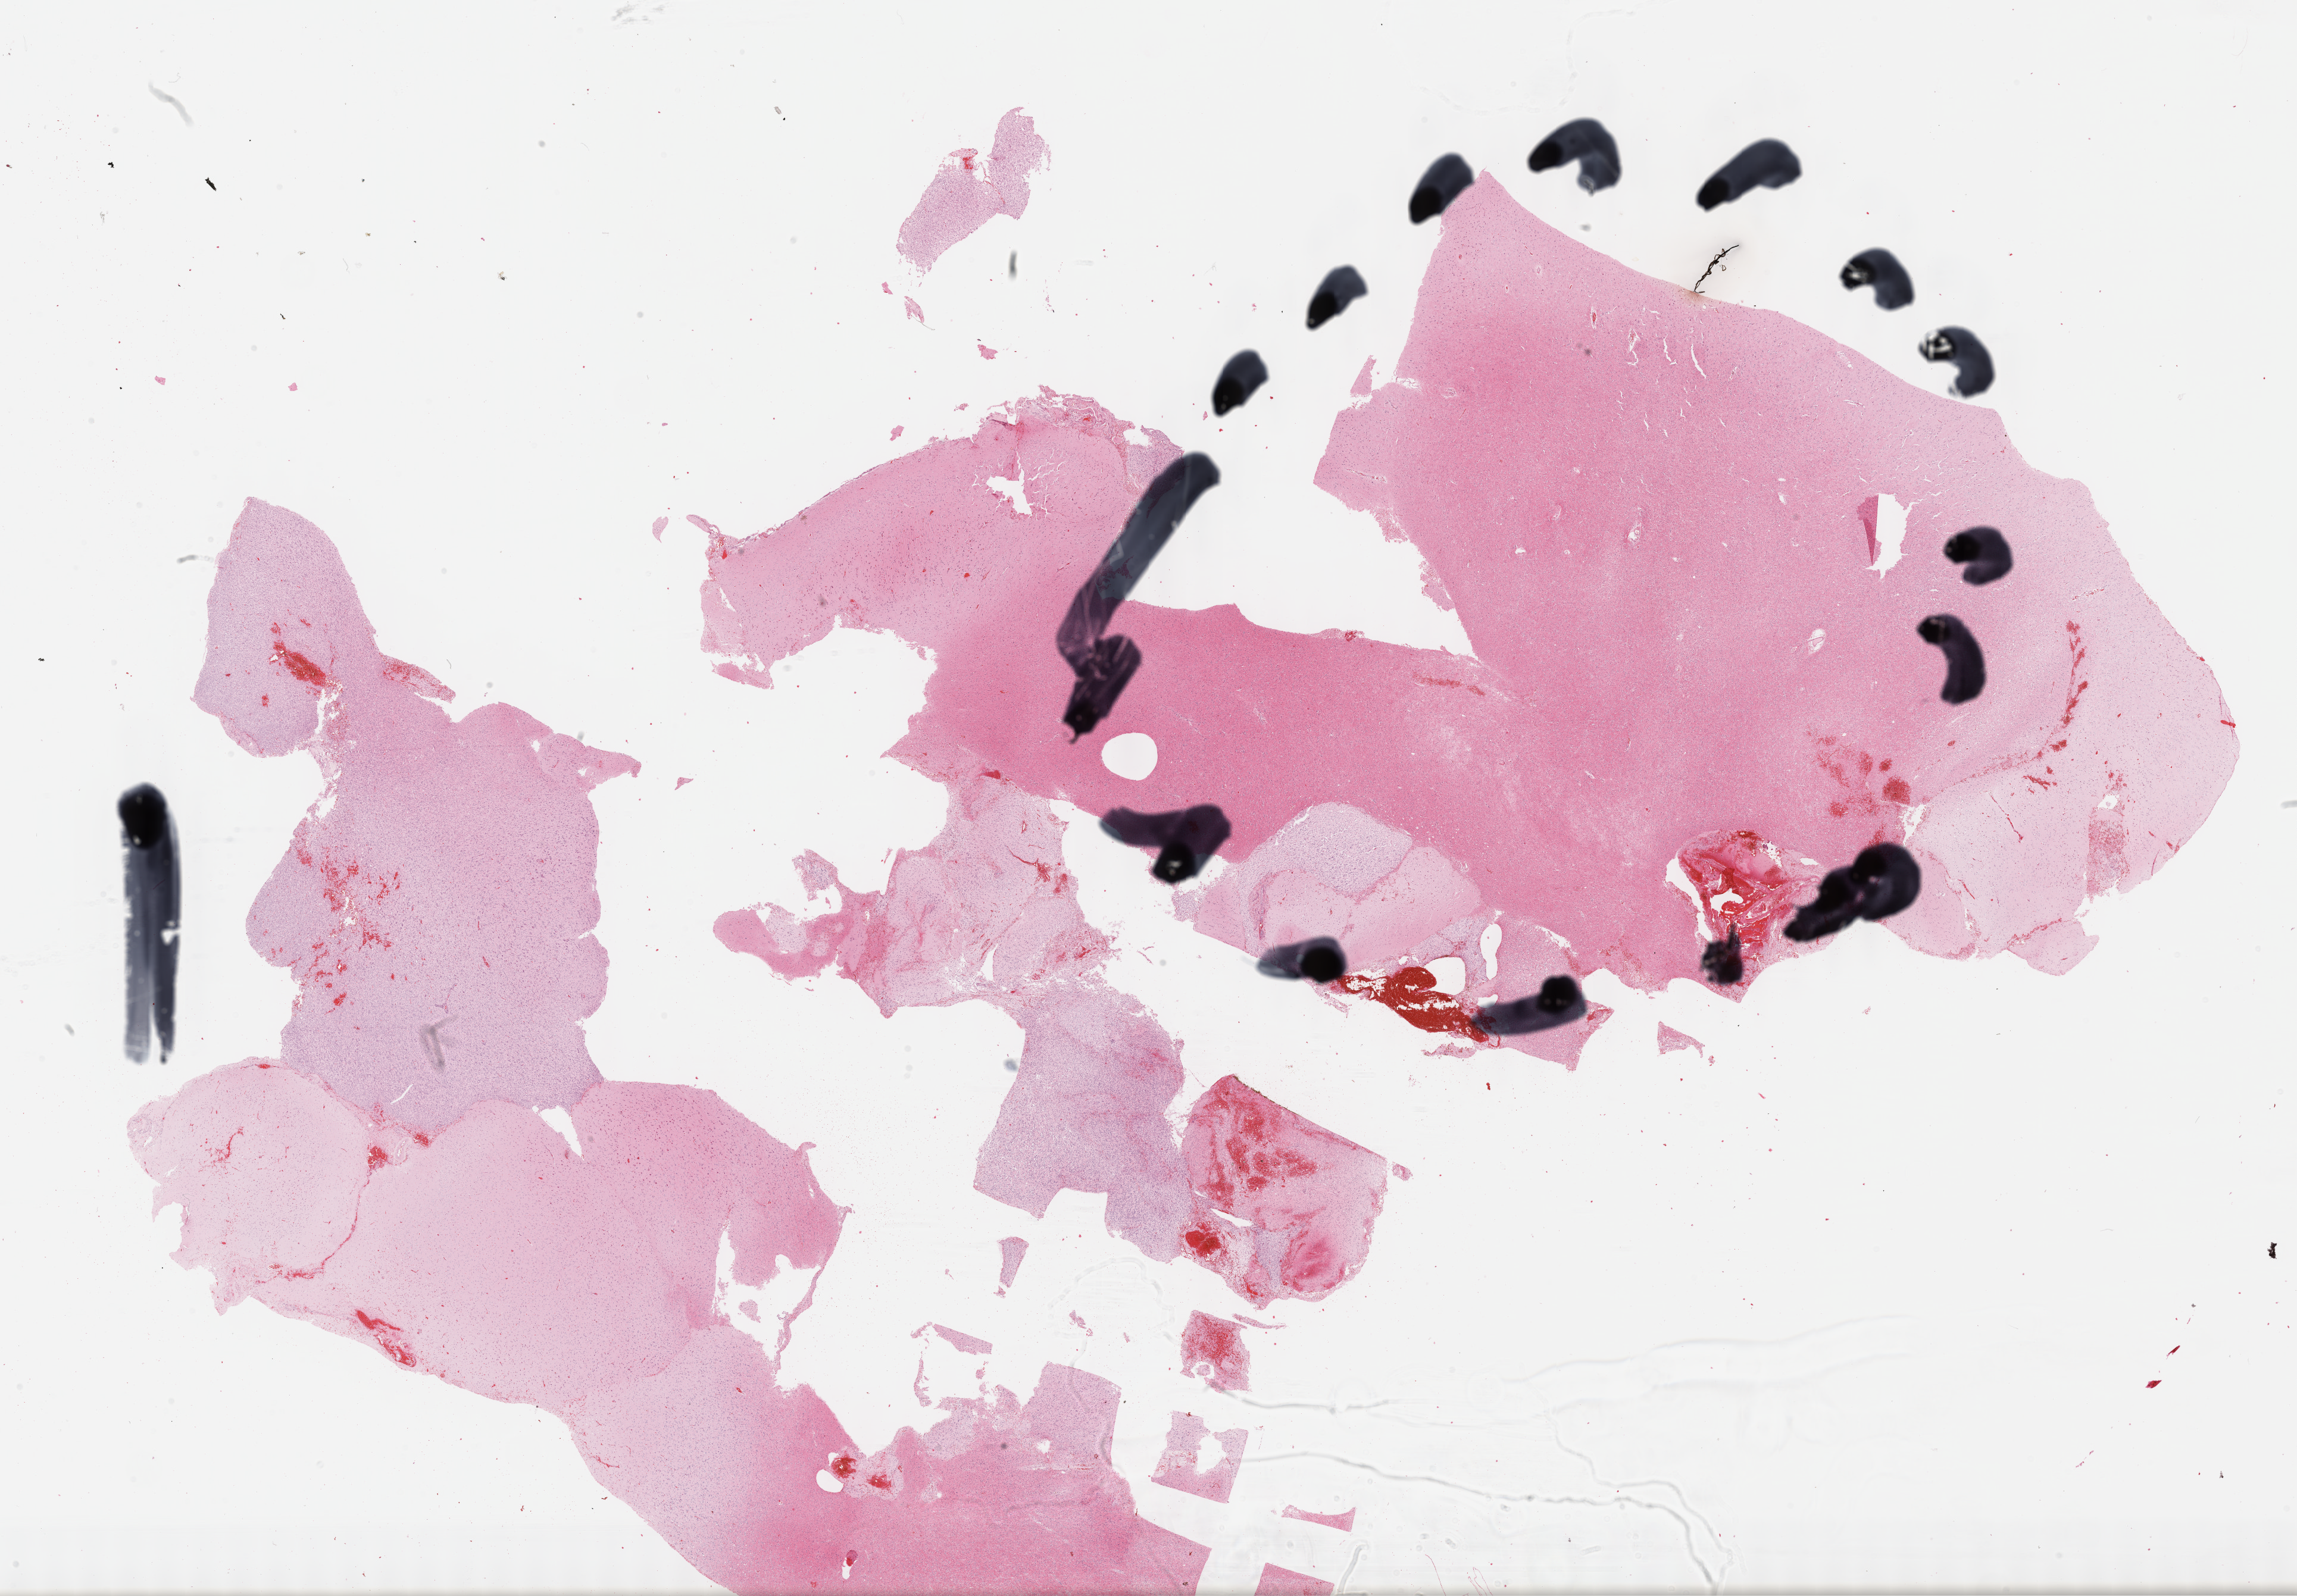
H&E-stained whole-slide image — shown as a low-resolution overview of the whole scanned area (about 31.2 x 21.7 mm). FFPE section. Primary tumour sample from the brain. Male patient; age at initial diagnosis 50 years. Histologic grade: G2 (moderately differentiated).
Laterality: left. Histologic diagnosis: Oligodendroglioma, NOS (cerebrum).